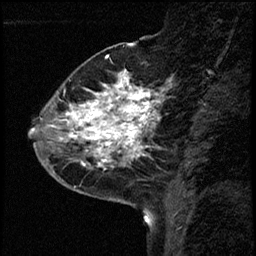
Breast MRI (dynamic contrast-enhanced), one sagittal slice; position 19 of 68 along the scan axis; dynamic contrast-enhanced study with each time point stored as its own series, time point 2 of 3 at this slice position (early post-contrast, ordered by acquisition time); 1.5 T; TE 4.2 ms, TR 17.6 ms; 2 mm slice thickness; 256 × 256 image matrix, field of view 200 × 200 mm. Patient: female, 52 years. From the clinical record (not read from this slice): setting: breast cancer imaged before/during neoadjuvant chemotherapy; receptor status: HER2-positive.
Annotated regions visible in this slice (semi-automatically segmented with operator editing):
- analysis volume of interest (the breast-tissue region the enhancement analysis was run in; not a lesion): bounding box <50,61,171,184> (left, top, right, bottom; pixels)
- tumour enhancement mask (voxels above the 100 % enhancement threshold inside the analysis volume of interest): <50,73,163,167>